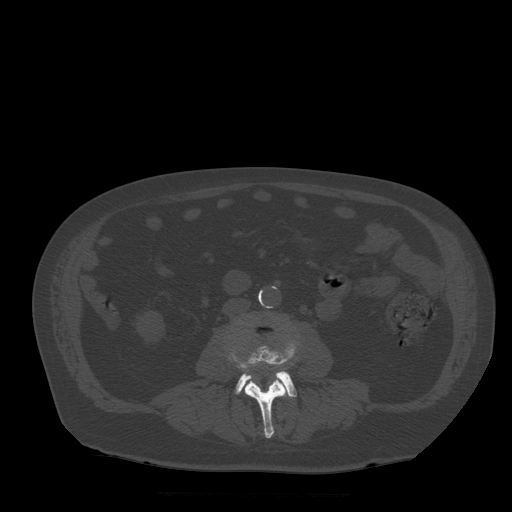
CT including the spine, one axial slice. Slice 131 of 522 in the series (ordered by position). Bone window (W 1800 / L 400 HU). 512 × 512 image matrix, field of view 420 × 420 mm. Patient age 72 years. Case-level facts recorded for this patient, not image findings: primary cancer: prostate.
Outlined on this slice (semi-automatic segmentation, software-assisted and operator-edited):
- L3 vertebra: box from (x=231, y=347) to (x=289, y=439) px
- L4 vertebra: (x=236, y=347)–(x=297, y=398)